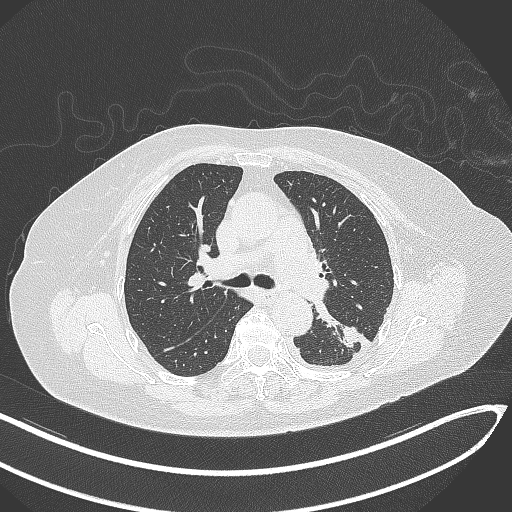
Chest CT, one axial slice. Slice 202 of 270 in the series (ordered by position). Lung window (W 1500 / L -600 HU). 1 mm slice thickness. 512 × 512 image matrix. Female patient, age 76 years. From the clinical record (not read from this slice): clinical TNM (as recorded): T1c N0 M0.
Outlined on this slice (rectangle marked by the reading radiologist):
- lung tumour (recorded histology: adenocarcinoma): bounding box <332,323,361,353> (left, top, right, bottom; pixels)